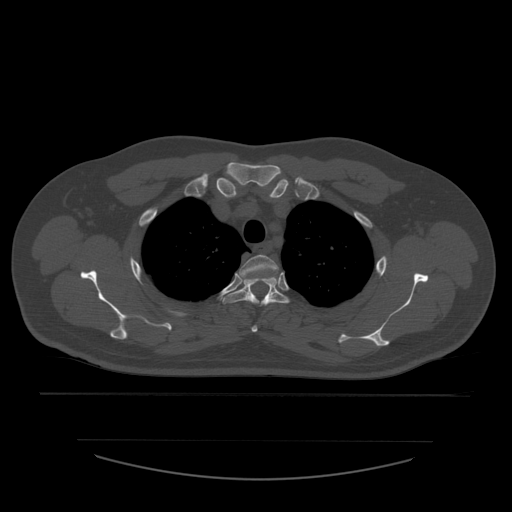
CT including the spine, one axial slice. Position 439 of 532 along the scan axis. 120 kVp. Bone window (W 1800 / L 400 HU). 1.25 mm slice thickness. 512 × 512 image matrix, field of view 441 × 441 mm. Patient age 44 years. Case-level facts recorded for this patient, not image findings: primary cancer: soft tissue sarcoma.
Annotated regions visible in this slice (semi-automatically segmented with operator editing):
- T2 vertebra: bounding box <240,255,279,333> (left, top, right, bottom; pixels)
- T3 vertebra: <221,274,289,307>